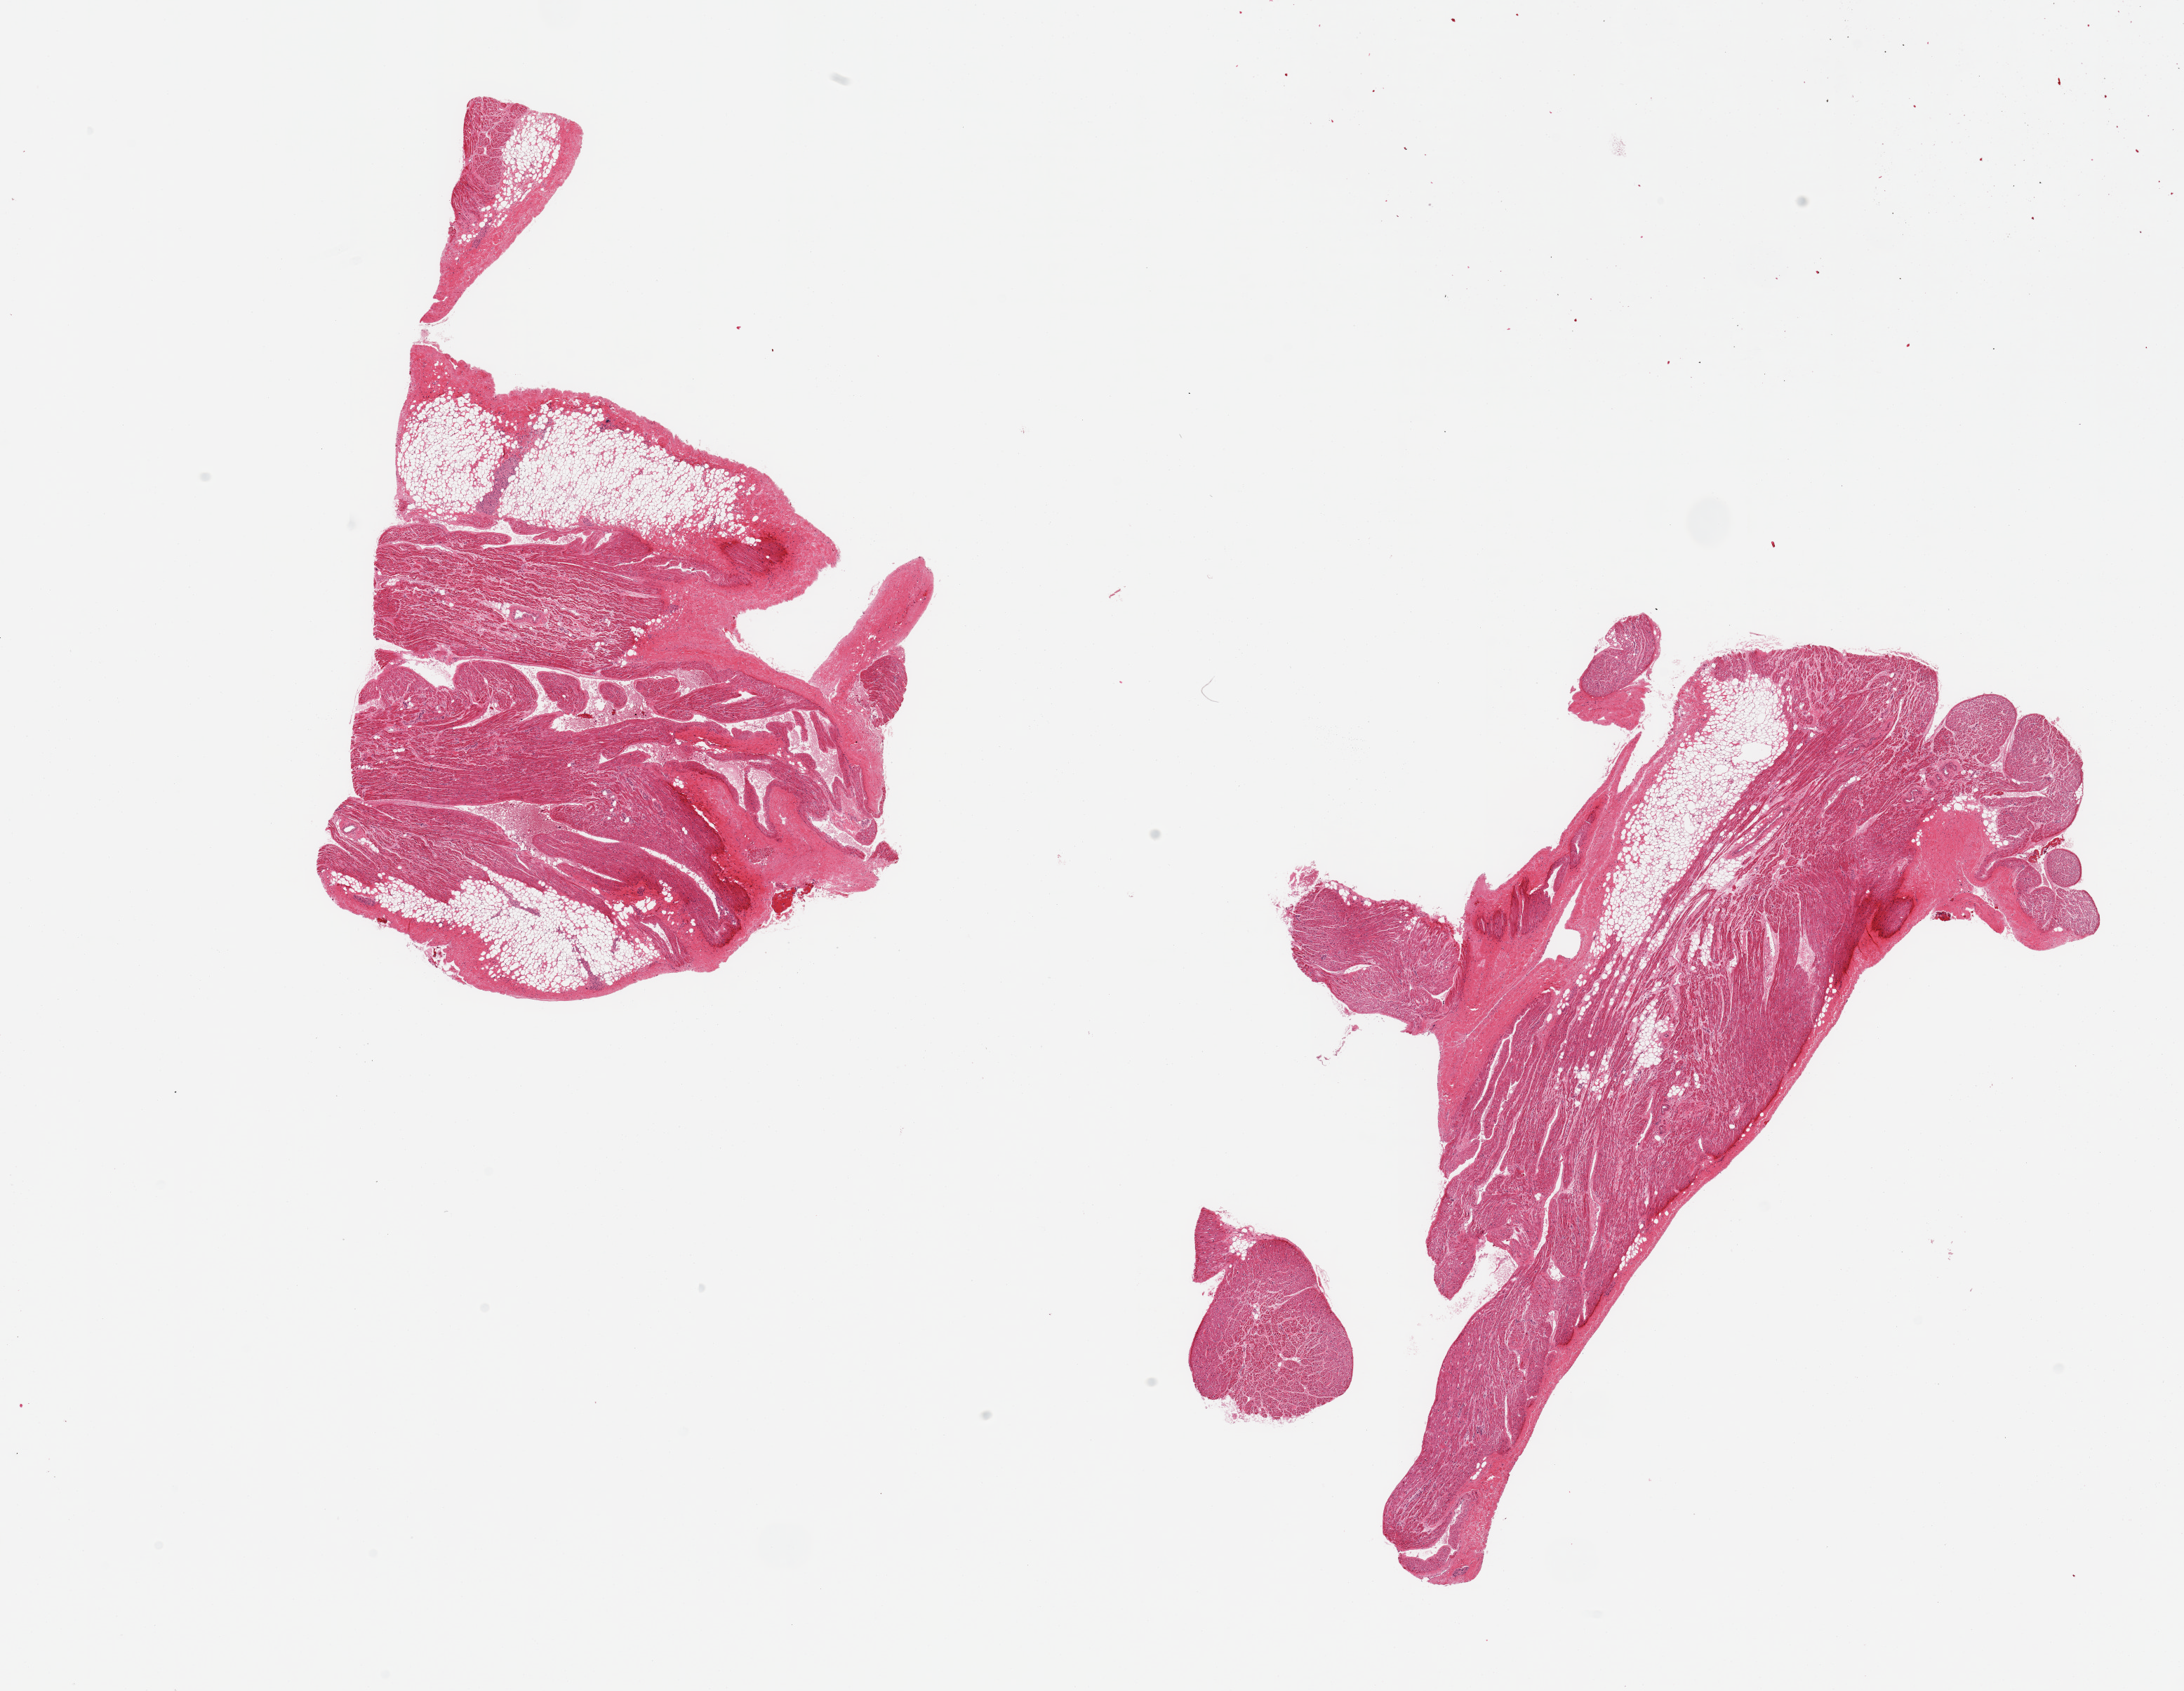
Whole-slide image, H&E stain, low-resolution overview of the scanned area, about 24.6 x 19.1 mm. PAXgene-fixed paraffin-embedded (PFPE) section. Target tissue: auricular appendage. Tissue donor sample. Donor: male.
- review note (as recorded): 3 pieces; 20 and 40% fibrous and fatty